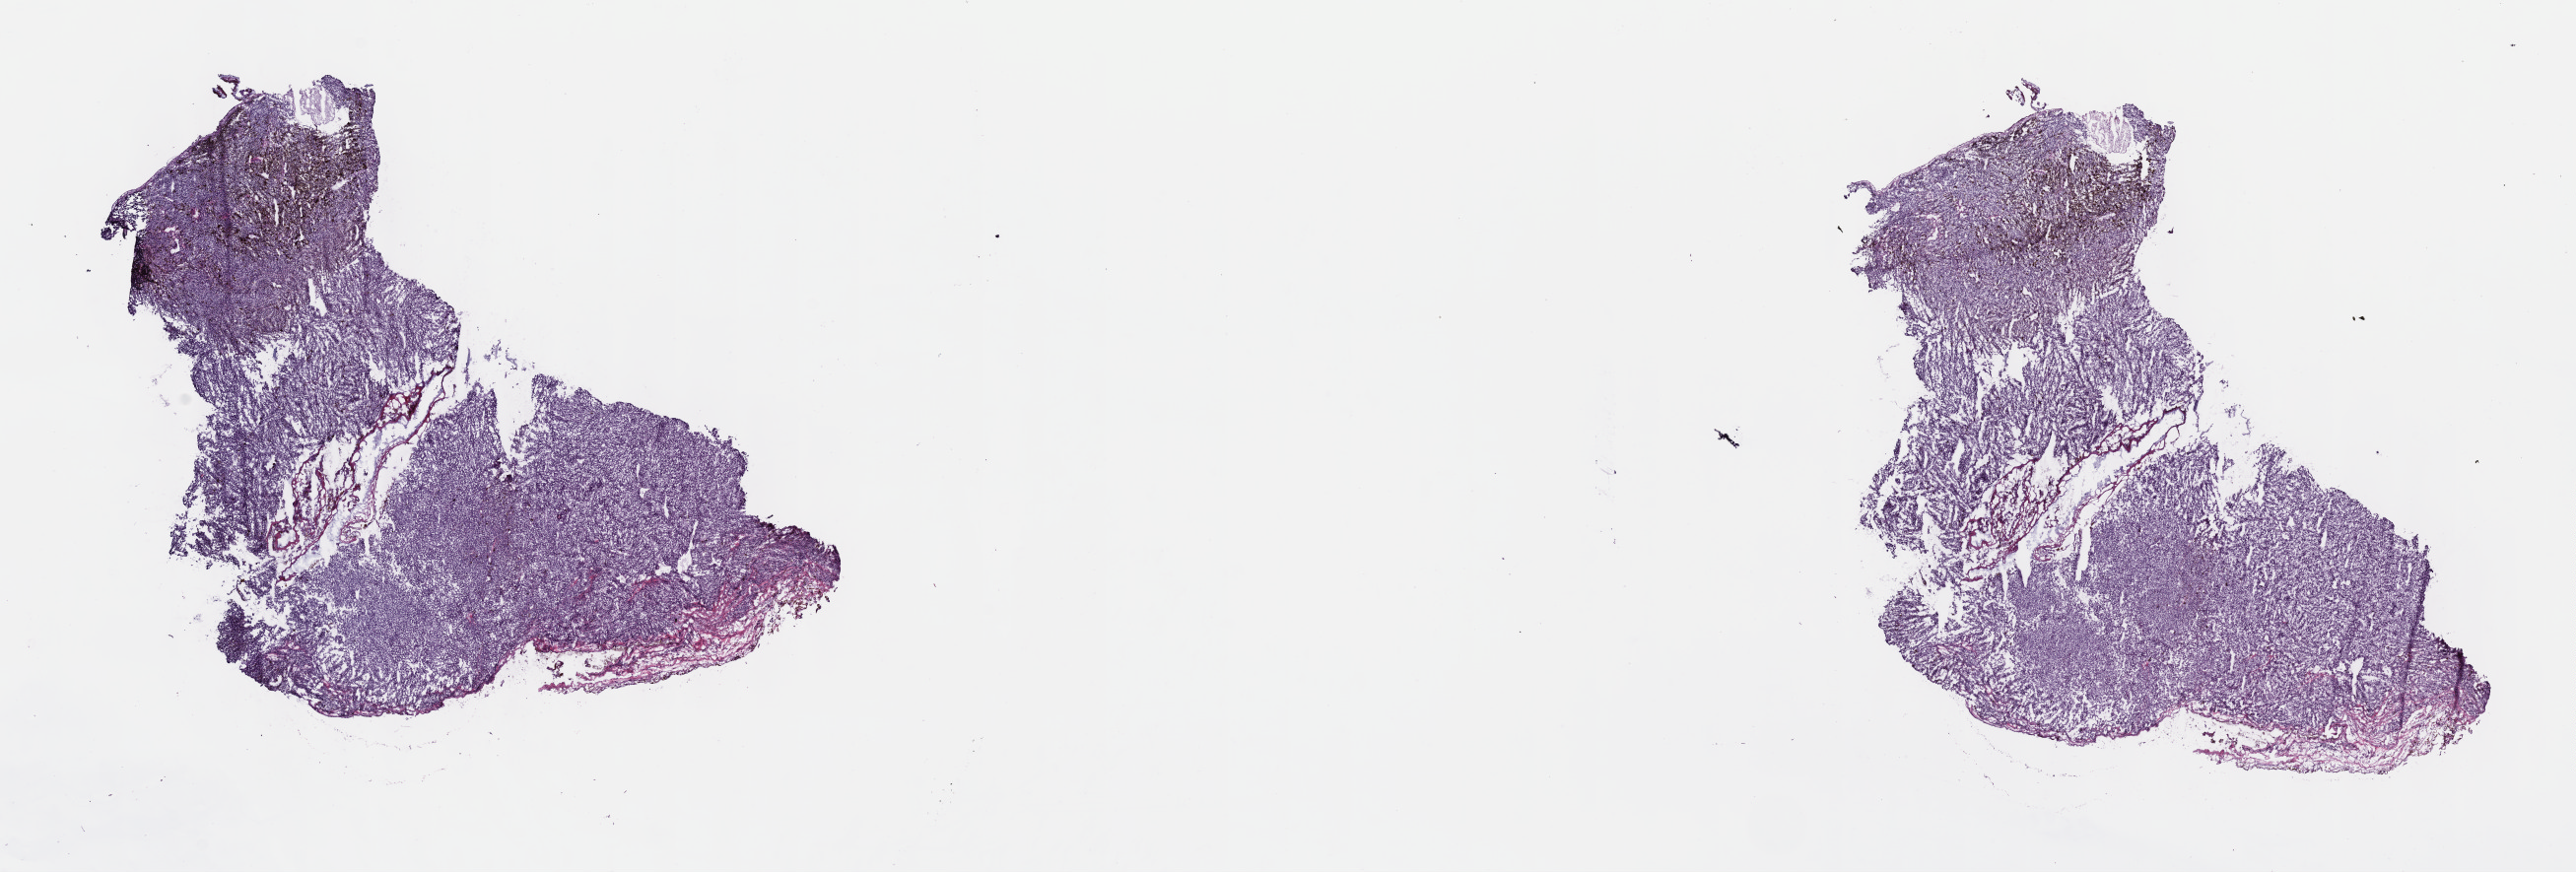
Hematoxylin and eosin (H&E) stained whole-slide image — a low-resolution overview of the entire scanned area, about 21.1 x 7.2 mm (from a 40x scan), frozen section, sample: primary tumour, uvea. Patient: male, age at initial diagnosis 64 years. Pathologist review of this section (percent, as recorded): tumour cells 100%, tumour nuclei 80%, normal cells 0%, stromal cells 0%, necrosis 0%. Inflammatory infiltration, as recorded: lymphocyte infiltration 1%, monocyte infiltration 0%, neutrophil infiltration 0%.
AJCC pathologic stage: IIA. Diagnosis: Mixed epithelioid and spindle cell melanoma (choroid).